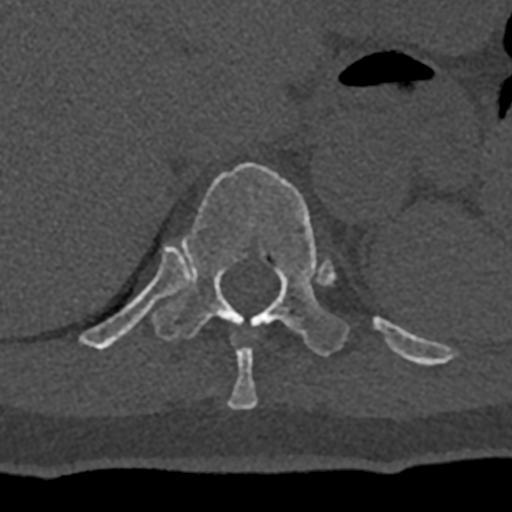
CT including the spine, one axial slice. Position 558 of 797 along the scan axis. Reconstruction kernel Br40s/3. Bone window (W 1800 / L 400 HU). 512 × 512 image matrix, field of view 160 × 160 mm. Patient: male, 74 years. Case-level facts recorded for this patient, not image findings: primary cancer: renal.
Structures marked on this image (semi-automatic segmentation, software-assisted and operator-edited):
- T10 vertebra: box from (x=227, y=337) to (x=258, y=409) px
- T11 vertebra: (x=79, y=163)–(x=432, y=366)